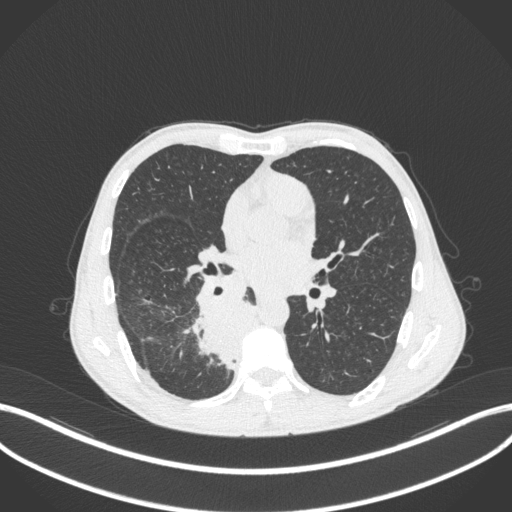
Chest CT, one axial slice; position 189 of 371 along the scan axis; reconstruction kernel B31f; 120 kVp; lung window (W 1500 / L -600 HU); 1 mm slice thickness; 512 × 512 image matrix. Patient: male, 58 years. Case-level facts recorded for this patient, not image findings: clinical TNM (as recorded): T3 N1 M1.
Structures marked on this image (rectangle marked by the reading radiologist):
- lung tumour (recorded histology: squamous cell carcinoma): box from (x=186, y=293) to (x=270, y=369) px